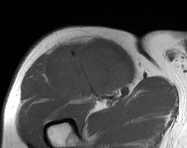
MRI of an extremity soft-tissue mass, one axial slice. Slice 102 of 114 in the series (ordered by position). MR volume resampled by the dataset authors to the PET/CT grid (not the native acquisition matrix). 187 × 148 image matrix, field of view 183 × 145 mm. Male patient. Case-level facts recorded for this patient, not image findings: histological type: pleiomorphic leiomyosarcoma; grade: intermediate; site of the primary tumour: right thigh.
Structures marked on this image (expert contour drawn on MRI and transferred to this co-registered scan by the dataset authors):
- gross tumour volume including surrounding oedema: bounding box [x1, y1, x2, y2] px = [57, 38, 130, 101]
- gross tumour volume (mass): [59, 40, 130, 101]